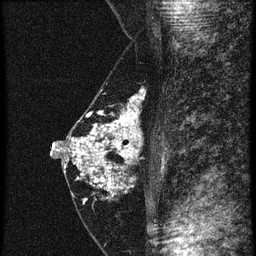
Breast MRI (dynamic contrast-enhanced), one sagittal slice. Position 26 of 60 along the scan axis. 4 images stored at this slice position (order not interpretable as contrast timing). 1.5 T. TE 4.2 ms, TR 20.4 ms. 1.5 mm slice thickness. 256 × 256 image matrix, field of view 180 × 180 mm. Patient: female, 46 years. Case-level facts recorded for this patient, not image findings: setting: breast cancer imaged before/during neoadjuvant chemotherapy; receptor status: triple-negative.
Annotated regions visible in this slice (semi-automatically segmented with operator editing):
- analysis volume of interest (the breast-tissue region the enhancement analysis was run in; not a lesion): bounding box [x1, y1, x2, y2] px = [67, 92, 148, 201]
- tumour enhancement mask (voxels above the 90 % enhancement threshold inside the analysis volume of interest): [70, 96, 140, 201]